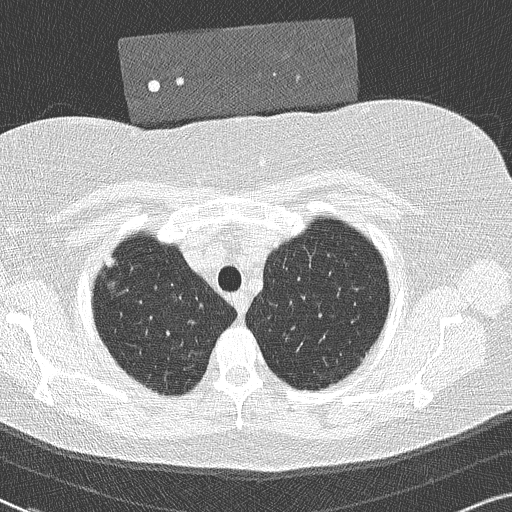
Chest CT (low-dose screening protocol), one axial image. Baseline screening round. Lung window (W 1500 / L -600 HU). 2 mm slice thickness. 120 kVp. Slice 38 of 306 in the series. 512 × 512 image matrix. Female, age 58 years at enrolment. Former smoker at enrolment.
Lesion marked by an expert reader, bounding box (x1, y1, x2, y2) in pixels: (94, 249, 131, 295). Screening reader's record for this exam: no non-calcified nodule ≥4 mm recorded. Participant outcome: lung cancer diagnosed 846 days after this screen (after the third annual screen) — bronchiolo-alveolar adenocarcinoma, NOS, right upper lobe, well differentiated (G1), stage IA (AJCC 6th edition), 9 mm at pathology.